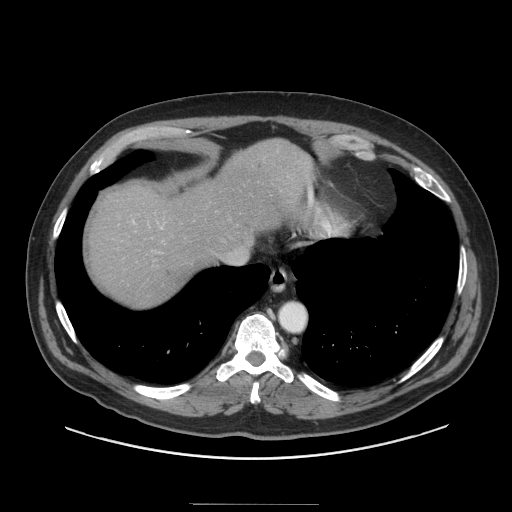
Contrast-enhanced abdominal CT (liver protocol), one axial slice. Slice 80 of 91 in the series (ordered by position). Reconstruction kernel STANDARD. Soft-tissue window (W 400 / L 40 HU). 2.5 mm slice thickness. 512 × 512 image matrix, field of view 440 × 440 mm. Case-level facts recorded for this patient, not image findings: diagnosis: hepatocellular carcinoma (patient treated with transarterial chemoembolisation; whether this scan precedes or follows treatment is not stated here); TNM stage (as recorded): Stage-I; Child-Pugh class: A; tumour size: 4 cm.
Annotated regions visible in this slice (semi-automatic segmentation, software-assisted and operator-edited):
- liver parenchyma outside the tumour (the mass and vessels are separate outlines, so this box may not span the whole liver): bounding box [x1, y1, x2, y2] px = [88, 138, 312, 306]
- liver vessels: [133, 221, 163, 229]